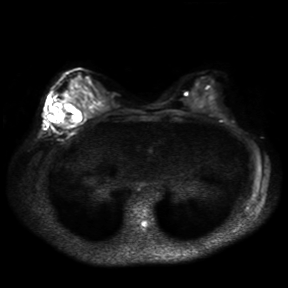
Breast MRI, one axial slice; position 16 of 30 along the scan axis; diffusion-weighted series; image 2 of 4 stored at this slice position (different b-values; order by instance number); 3 T; 4 mm slice thickness; 288 × 288 image matrix, field of view 360 × 360 mm. Female patient.
Structures marked on this image (manually delineated by an expert):
- tumour on diffusion-weighted imaging: box from (x=51, y=102) to (x=70, y=128) px